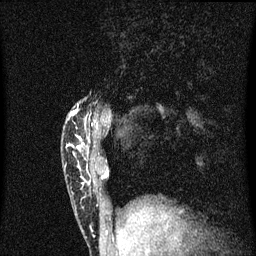
Breast MRI (dynamic contrast-enhanced), one sagittal slice. Slice 13 of 60 in the series (ordered by position). Dynamic contrast-enhanced series, image 2 of 3 at this slice position (ordered by acquisition). 1.5 T. TE 4.2 ms, TR 8.4 ms. 2 mm slice thickness. 256 × 256 image matrix, field of view 200 × 200 mm. Patient: female, 40 years.
Annotated regions visible in this slice (semi-automatic segmentation, software-assisted and operator-edited):
- analysis volume of interest (the breast-tissue region the enhancement analysis was run in; not a lesion): box from (x=64, y=104) to (x=102, y=203) px
- tumour enhancement mask (voxels above the 70 % enhancement threshold inside the analysis volume of interest): (x=70, y=110)–(x=87, y=149)